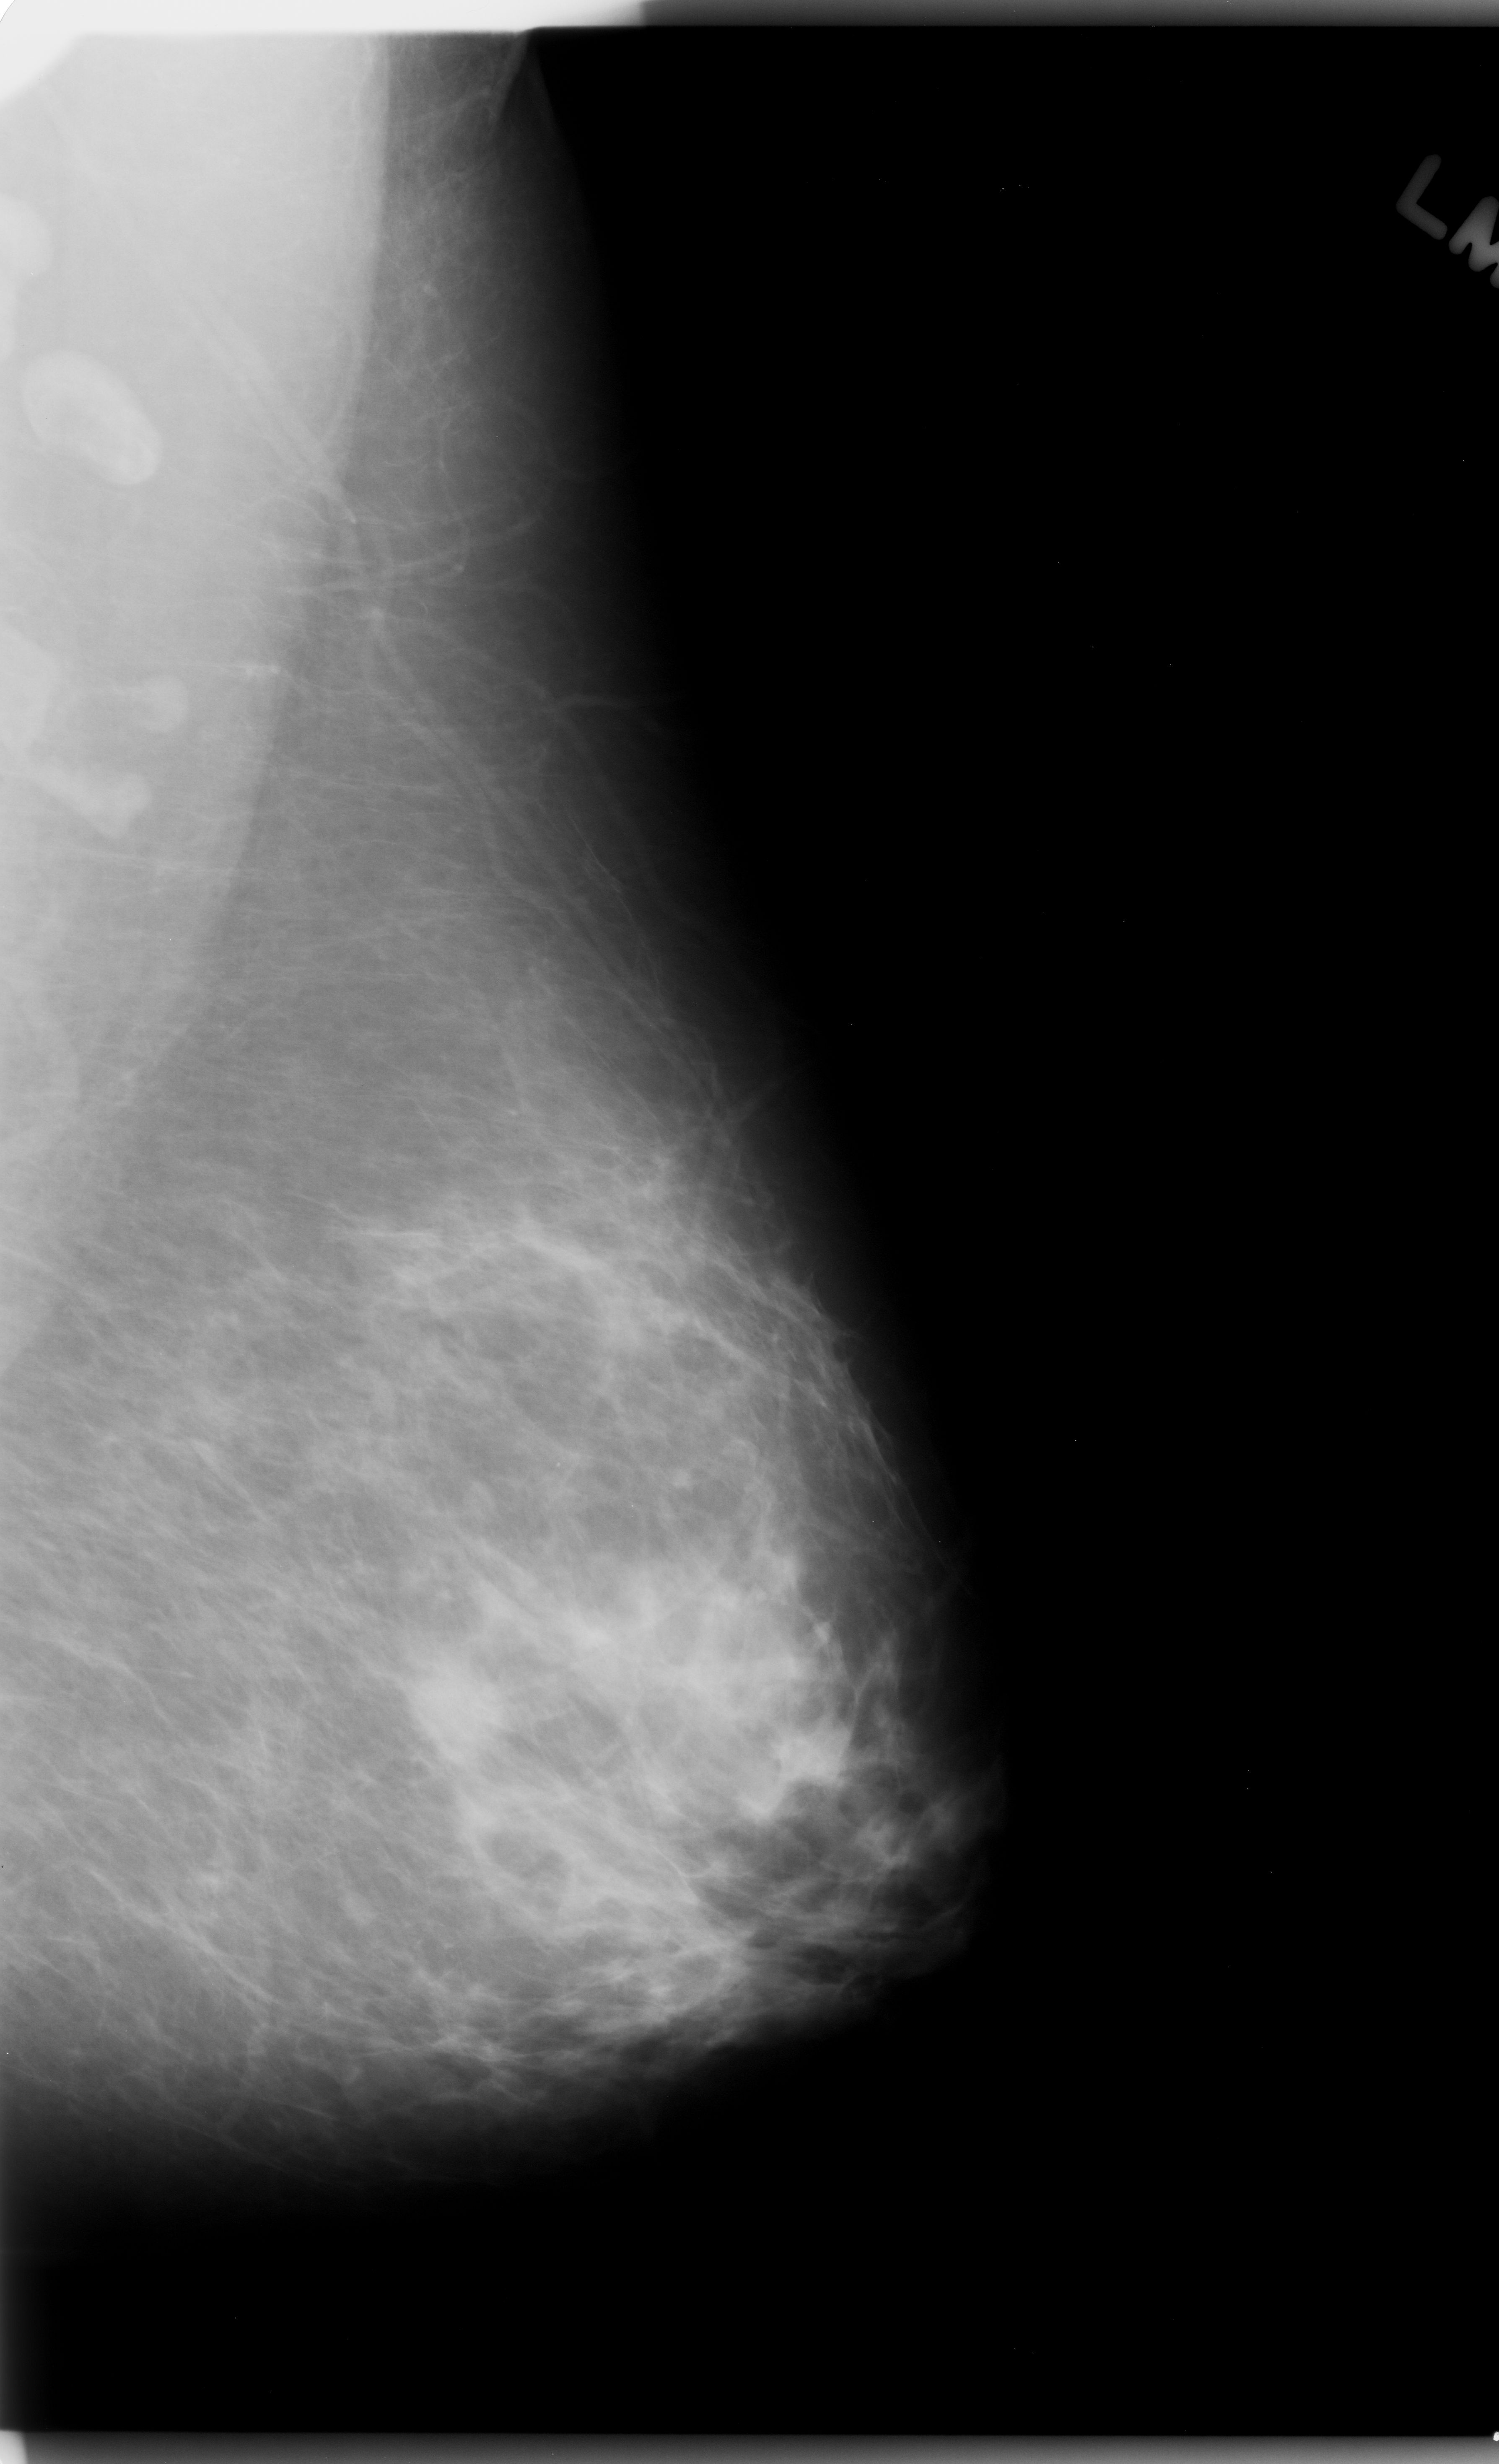
Scanned film-screen mammogram; left breast; MLO view; BI-RADS breast density category 2 (scale 1–4); 1499 × 2464 image matrix.
Expert-marked regions of interest on this image (one box per marked abnormality):
- mass, shape oval, margins microlobulated; BI-RADS assessment category 4; subtlety rating 5 on a 1 (subtle) to 5 (obvious) scale; pathology result (as recorded, not read from the image): malignant: box from (x=401, y=1646) to (x=533, y=1778) px